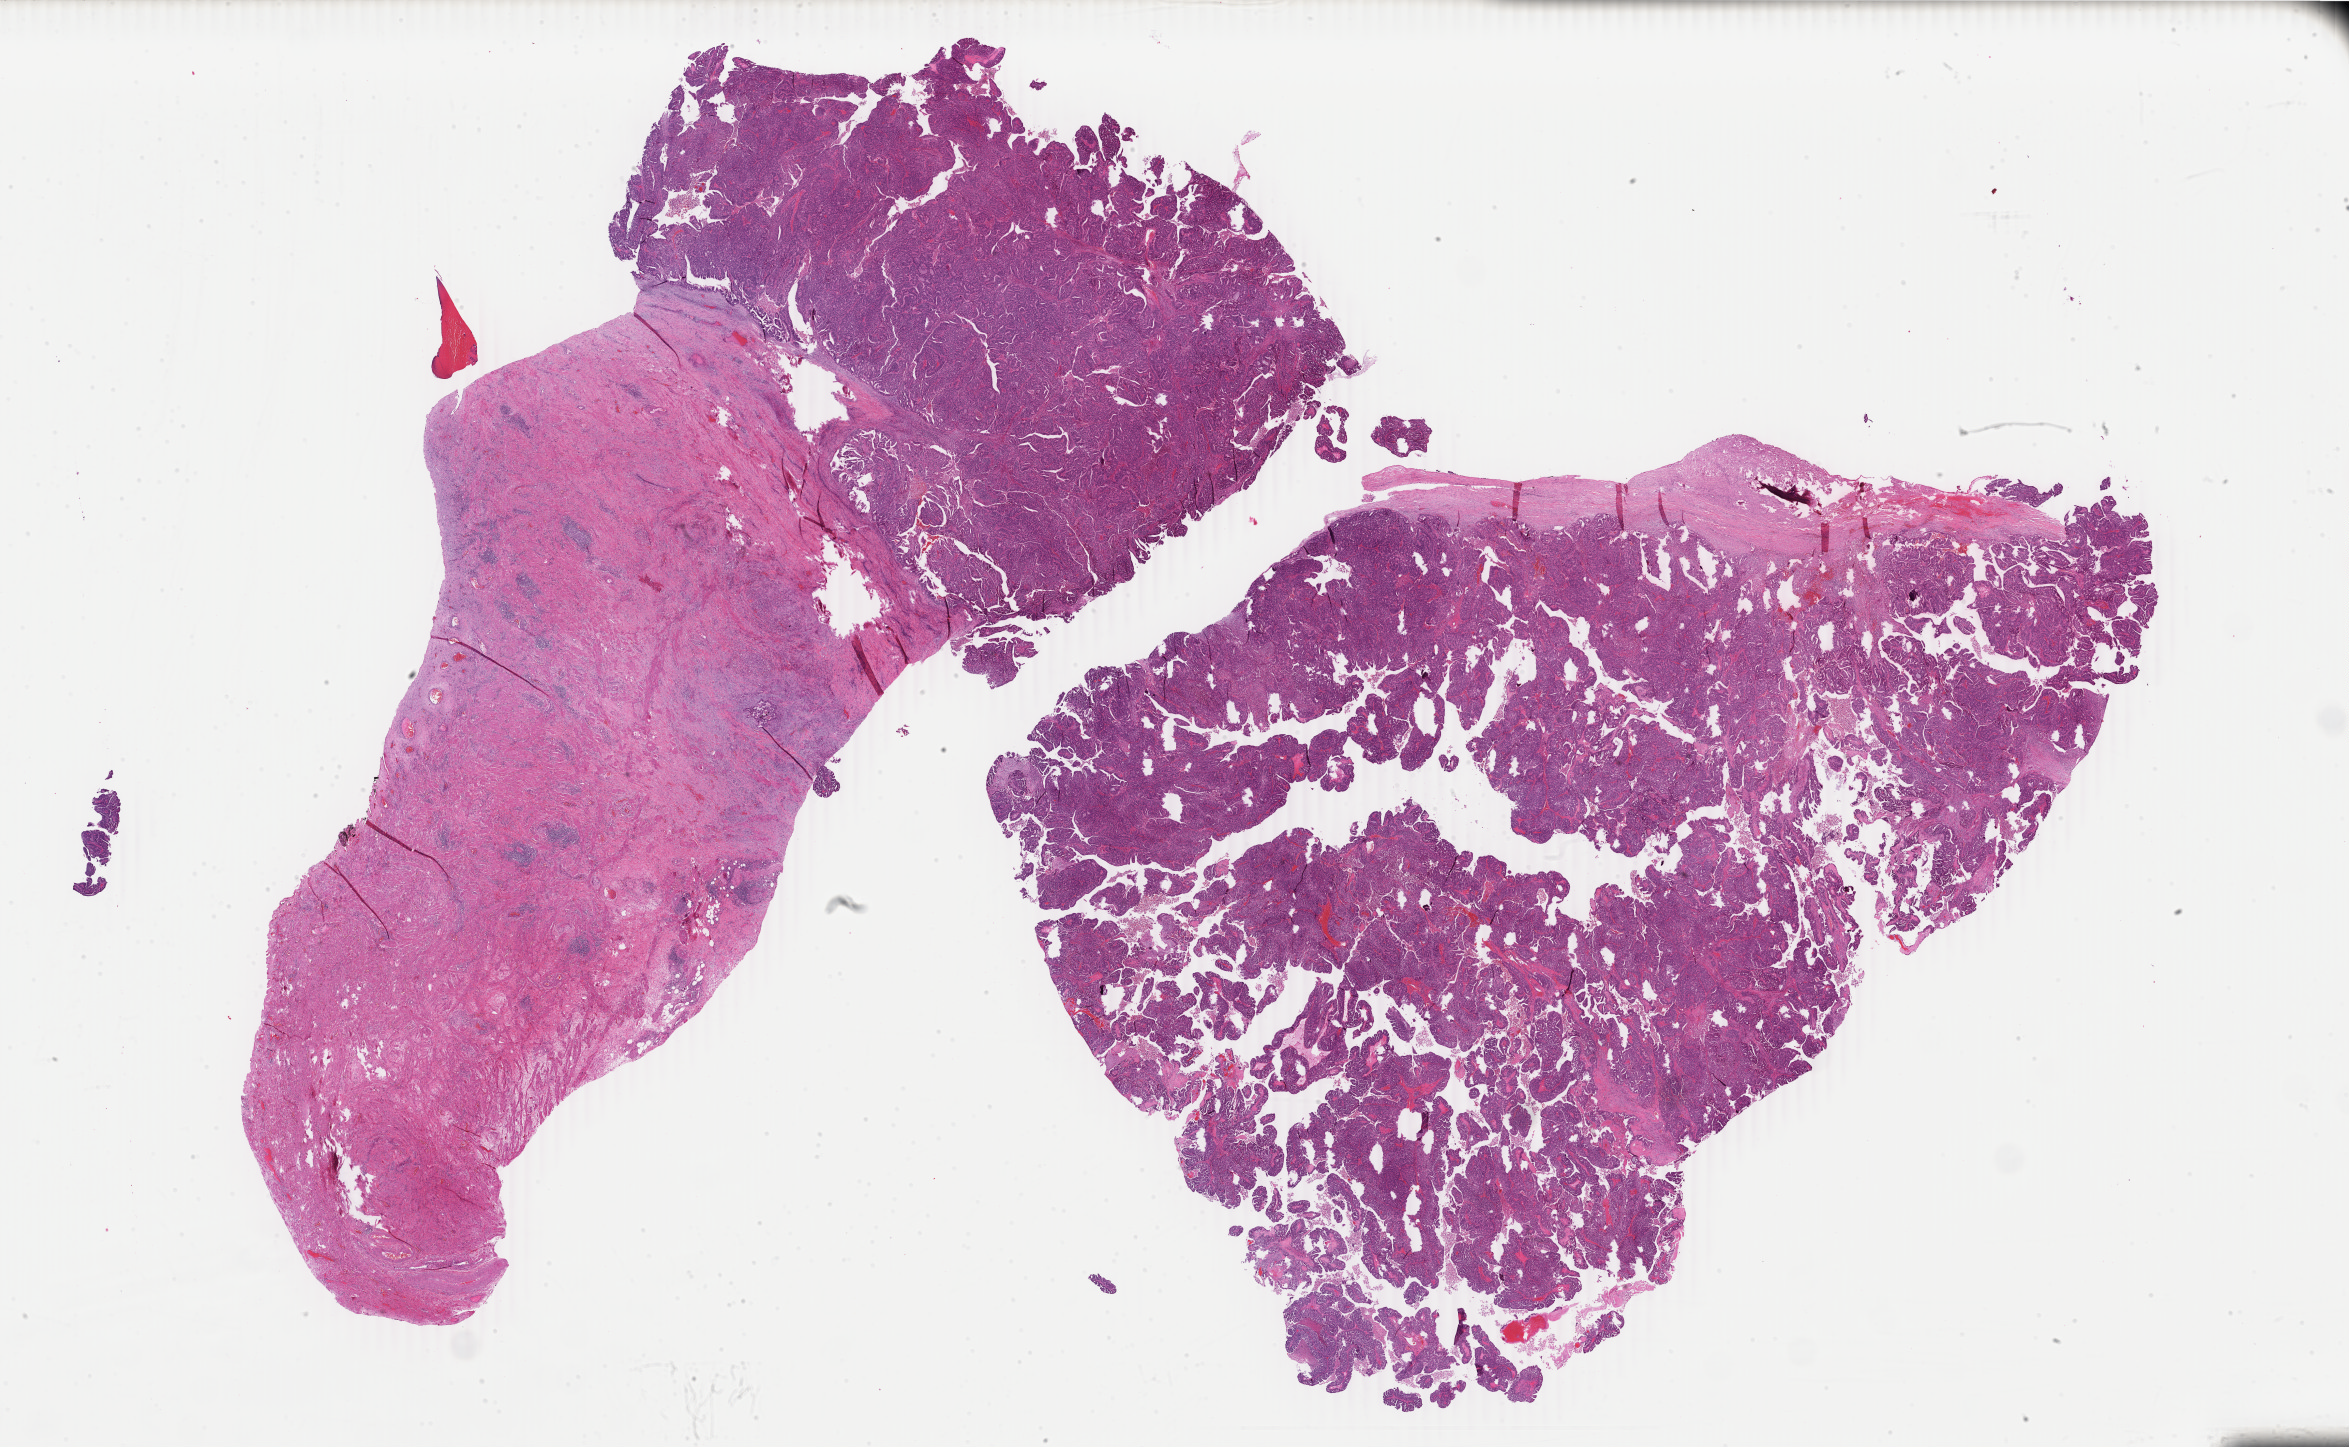
Whole-slide histology image, H&E-stained, low-resolution overview of the scanned area, about 37.4 x 23.0 mm (from a 40x scan). Formalin-fixed paraffin-embedded (FFPE) diagnostic section. Ovary, primary tumour sample. Female patient; age at initial diagnosis 55 years. Histologic grade: G3 (poorly differentiated).
• FIGO stage: IIB
• pathologic diagnosis: Cystadenocarcinoma, NOS
• laterality: left